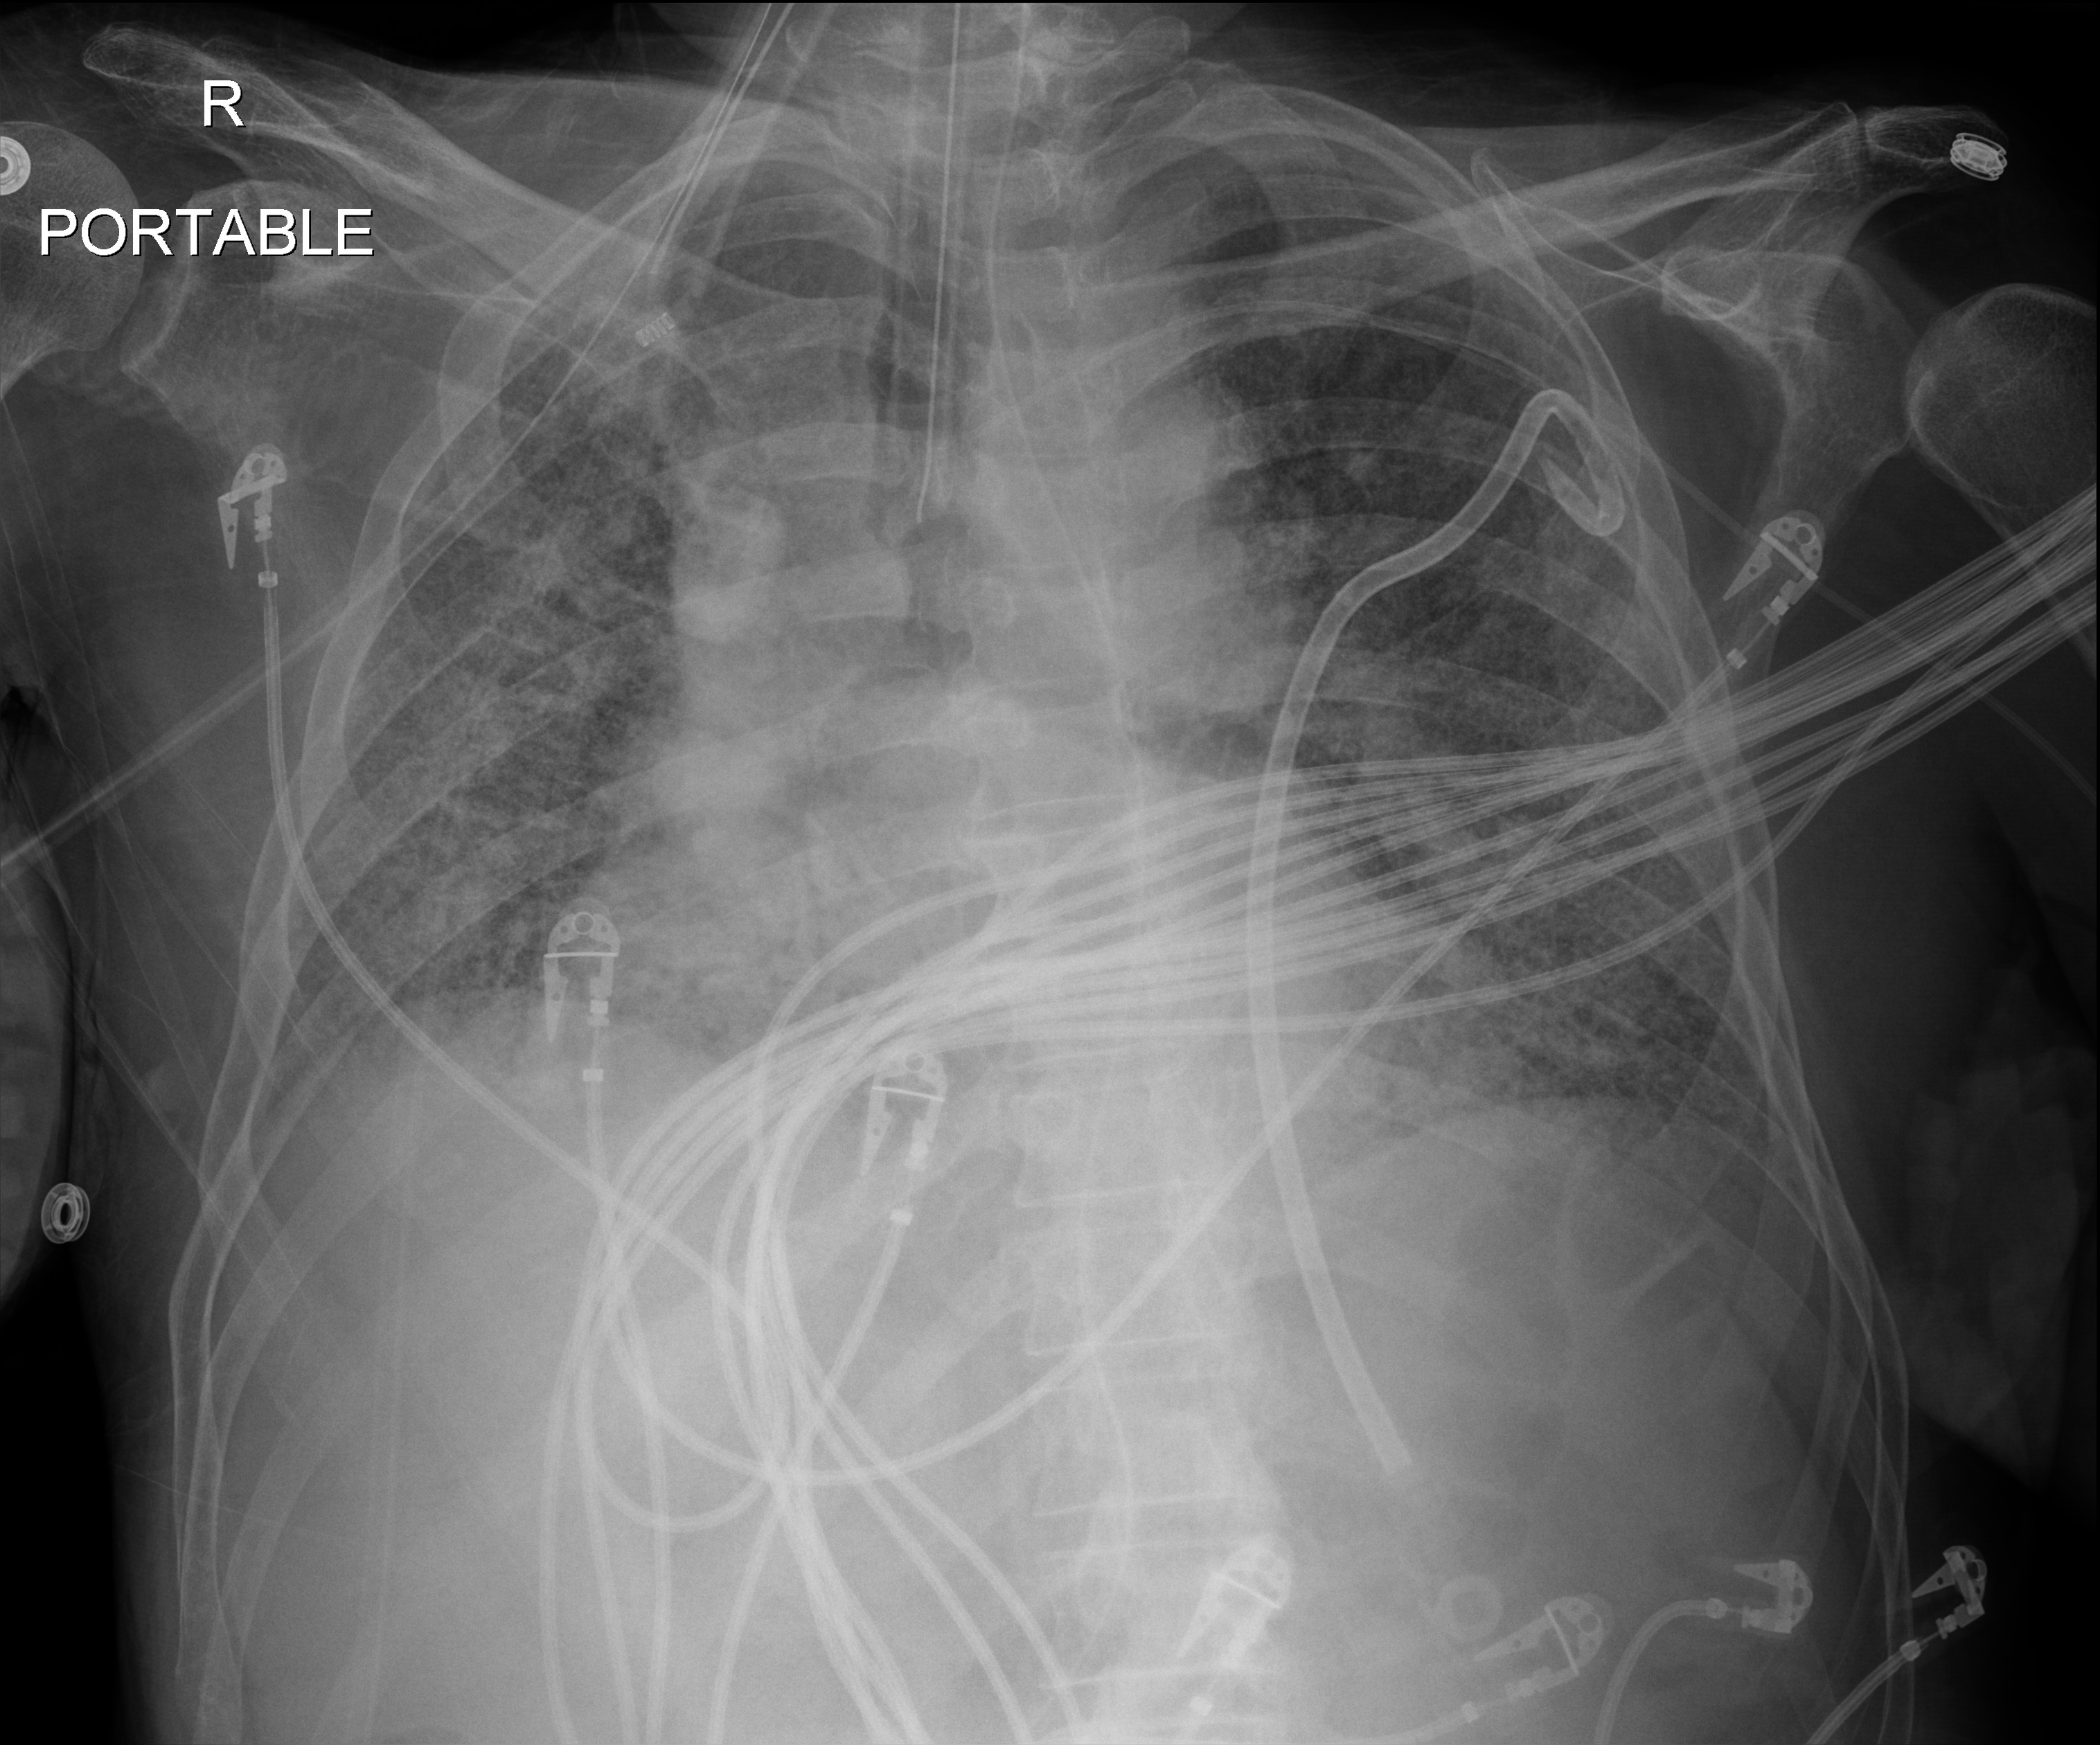
Chest radiograph (digital radiography); anteroposterior (AP) projection. Male patient hospitalised with COVID-19, age 60–74 years.
Hospital-stay facts (about this admission, not read from this image; timing relative to this image not recorded): mechanically ventilated during this hospital stay: yes.